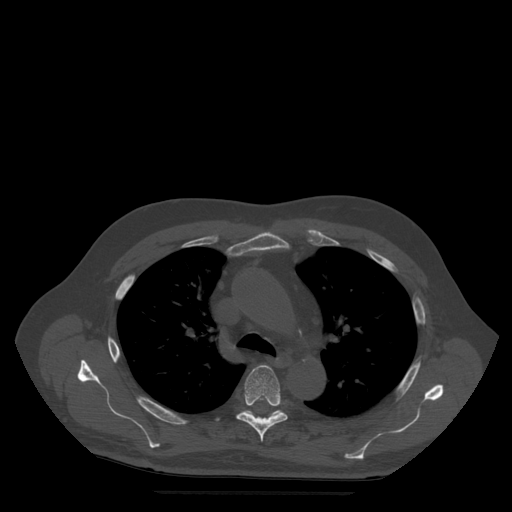
CT including the spine, one axial slice. Position 371 of 522 along the scan axis. Bone window (W 1800 / L 400 HU). 512 × 512 image matrix. Patient age 72 years. Case-level facts recorded for this patient, not image findings: primary cancer: prostate.
Annotated regions visible in this slice (semi-automatically segmented with operator editing):
- T5 vertebra: bounding box (x1, y1, x2, y2) in pixels: (237, 365, 288, 442)
- T6 vertebra: (246, 411, 278, 419)